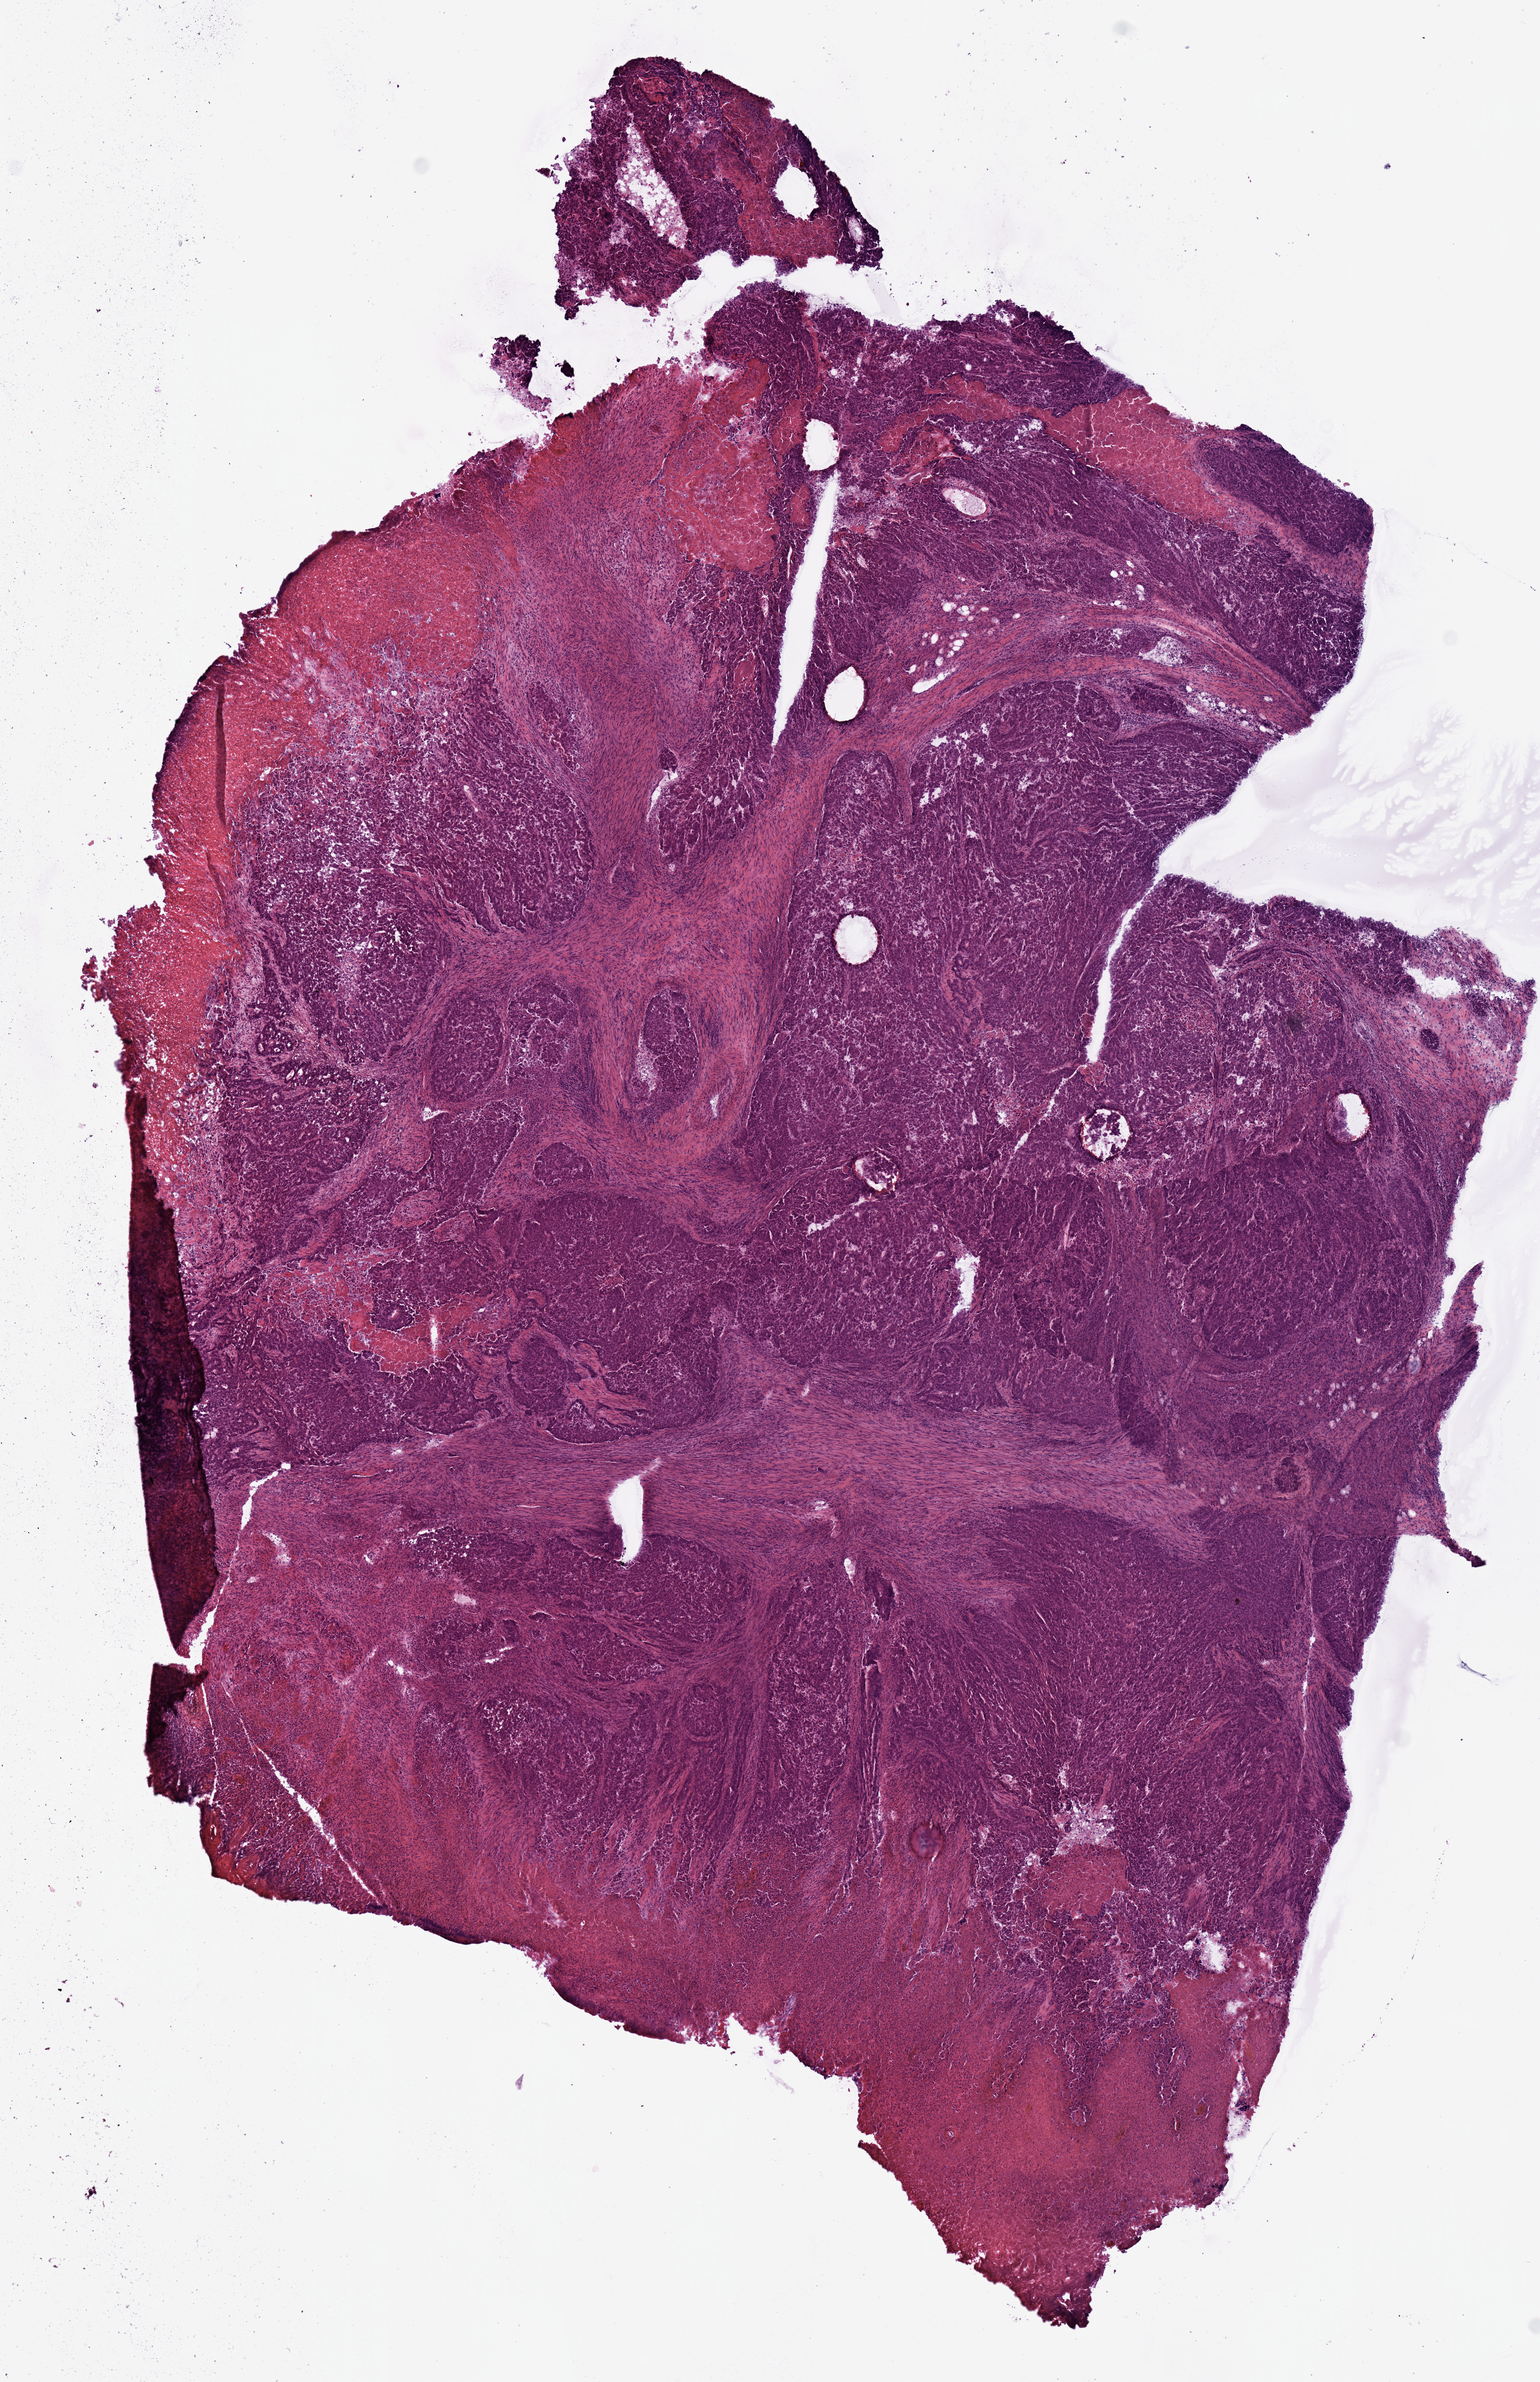
Hematoxylin and eosin (H&E) stained whole-slide image, low-resolution overview of the scanned area, about 7.9 x 12.2 mm, frozen section, sample: primary tumour, rectum. Male patient; age at initial diagnosis 57 years. Composition of this section per pathologist review: tumour cells 90%, tumour nuclei 75%, normal cells 0%, stromal cells 5%, necrosis 5%.
Histologic diagnosis: Adenocarcinoma, NOS. AJCC pathologic stage: IIA (7th edition). Lymph nodes positive (case pathology): 0 of 18 examined.